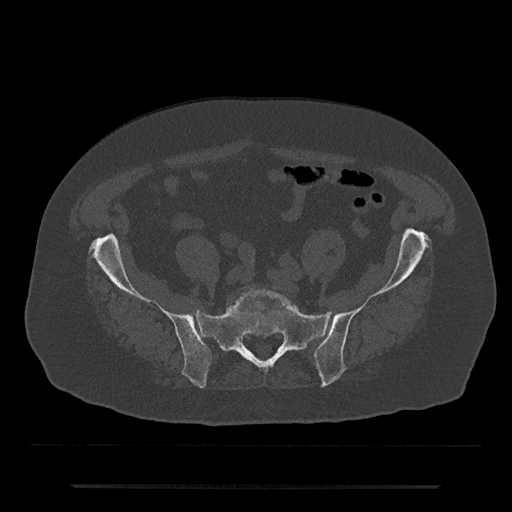
CT including the spine, one axial slice. Position 239 of 797 along the scan axis. 120 kVp. Bone window (W 1800 / L 400 HU). 512 × 512 image matrix, field of view 434 × 434 mm. Patient: male, 80 years. Case-level facts recorded for this patient, not image findings: primary cancer: prostate; vertebrae with lytic lesions (as recorded): L1, T11.
Outlined on this slice (semi-automatically segmented with operator editing):
- L5 vertebra: bounding box (x1, y1, x2, y2) in pixels: (232, 289, 299, 312)